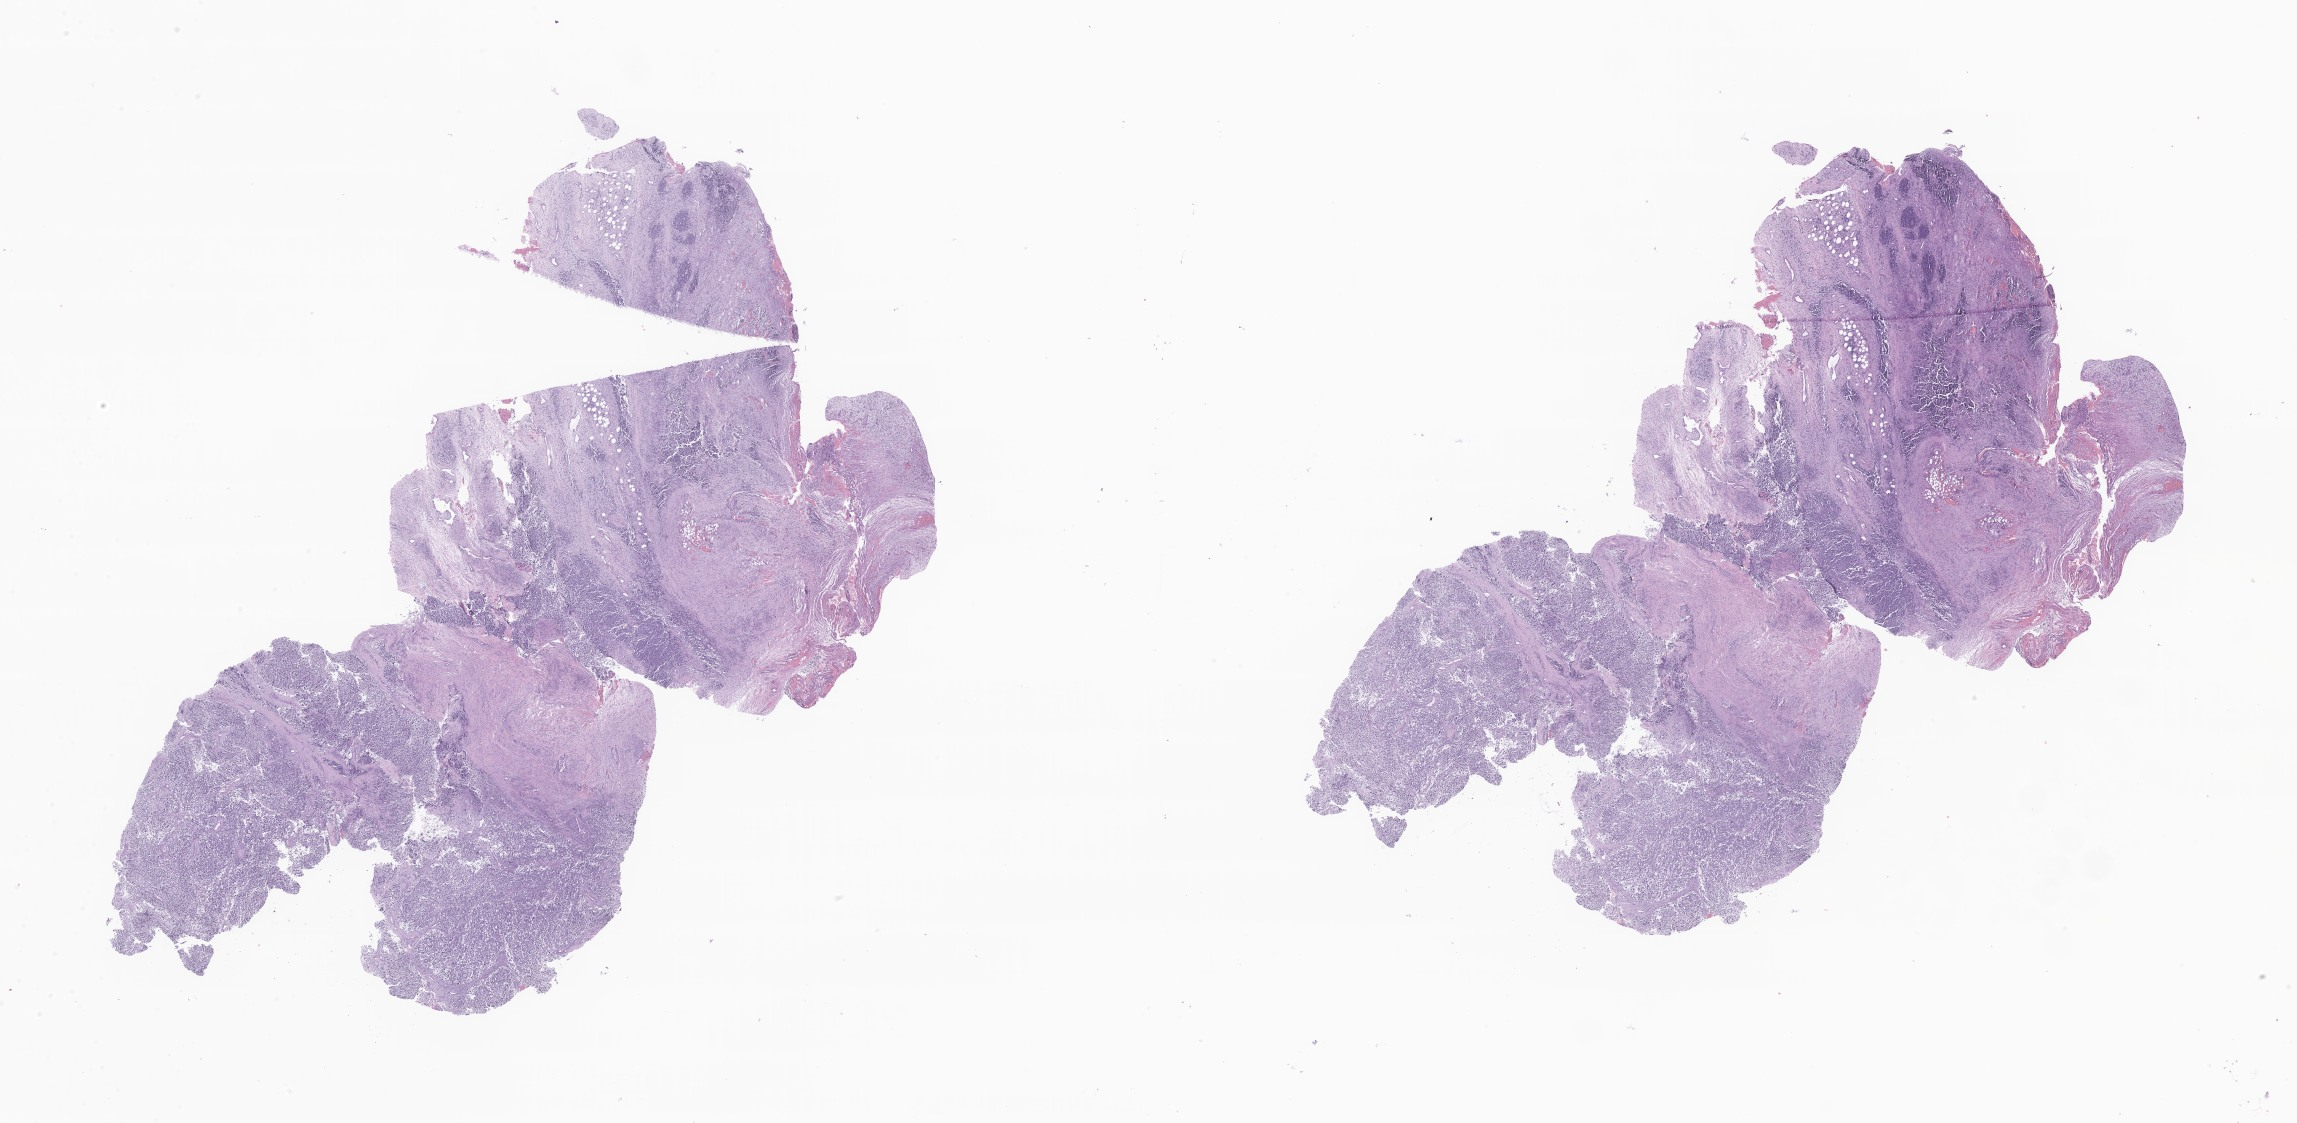
H&E whole-slide image of tumor tissue from the abdomen, low-resolution overview of the scanned area, about 38.7 x 18.9 mm. Formalin-fixed, paraffin-embedded (FFPE) tissue. Female patient, age 40 months.
• diagnosis: Rhabdomyosarcoma, NOS